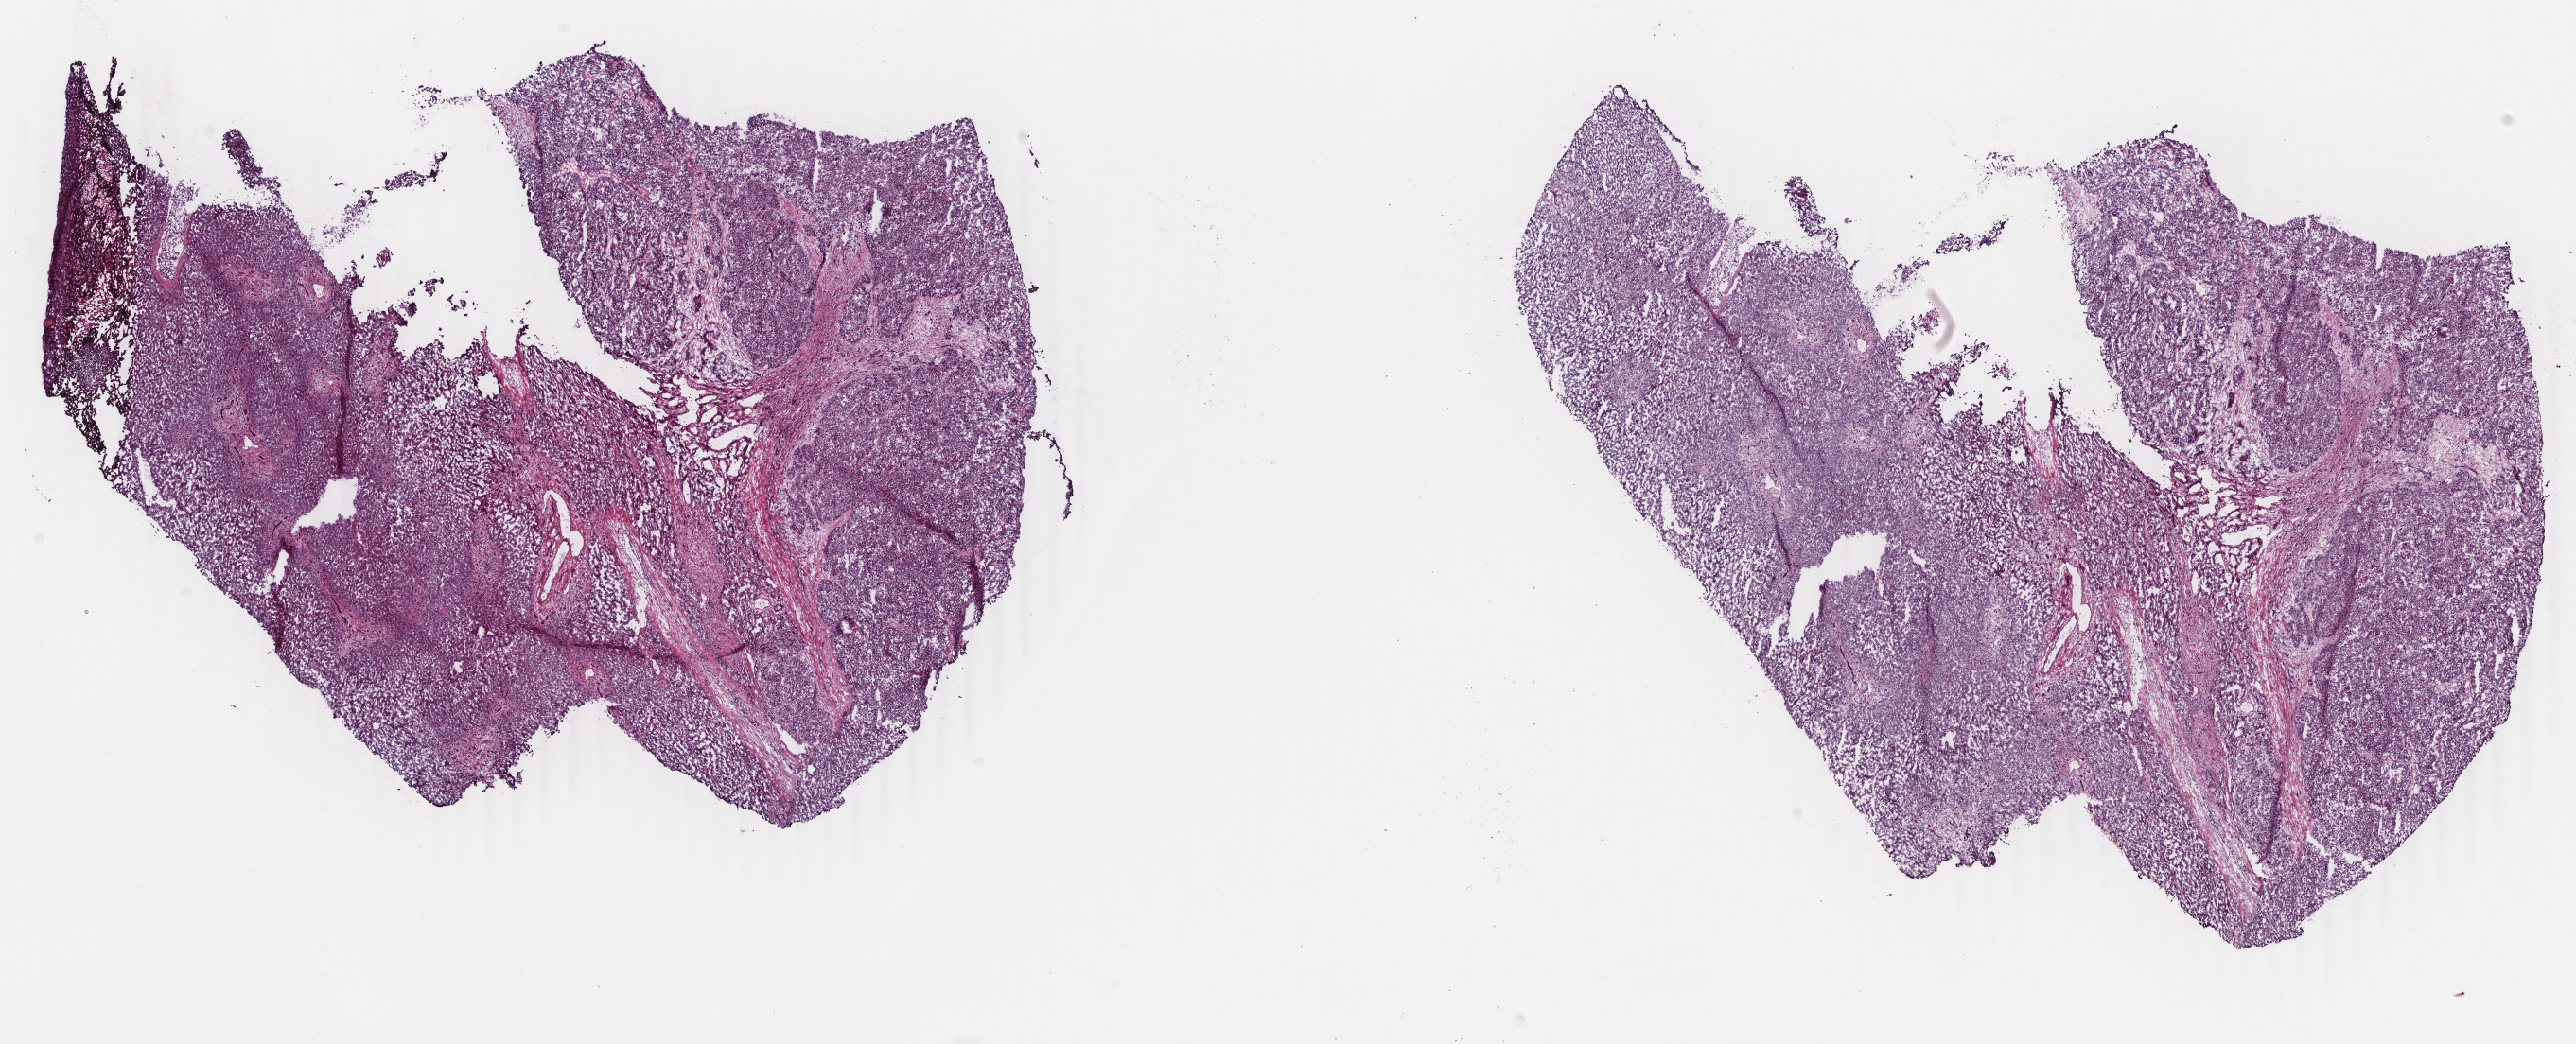
Whole-slide histology image, Hematoxylin and eosin (H&E) stained, low-resolution overview of the scanned area, about 21.7 x 8.8 mm (from a 40x scan), frozen section from the top of the tissue portion, primary tumour sample from the liver. Patient: female, age at initial diagnosis 52 years. Slide review estimates, as recorded: tumour cells 82%, tumour nuclei 85%.
Histologic diagnosis: Hepatocellular carcinoma, NOS.